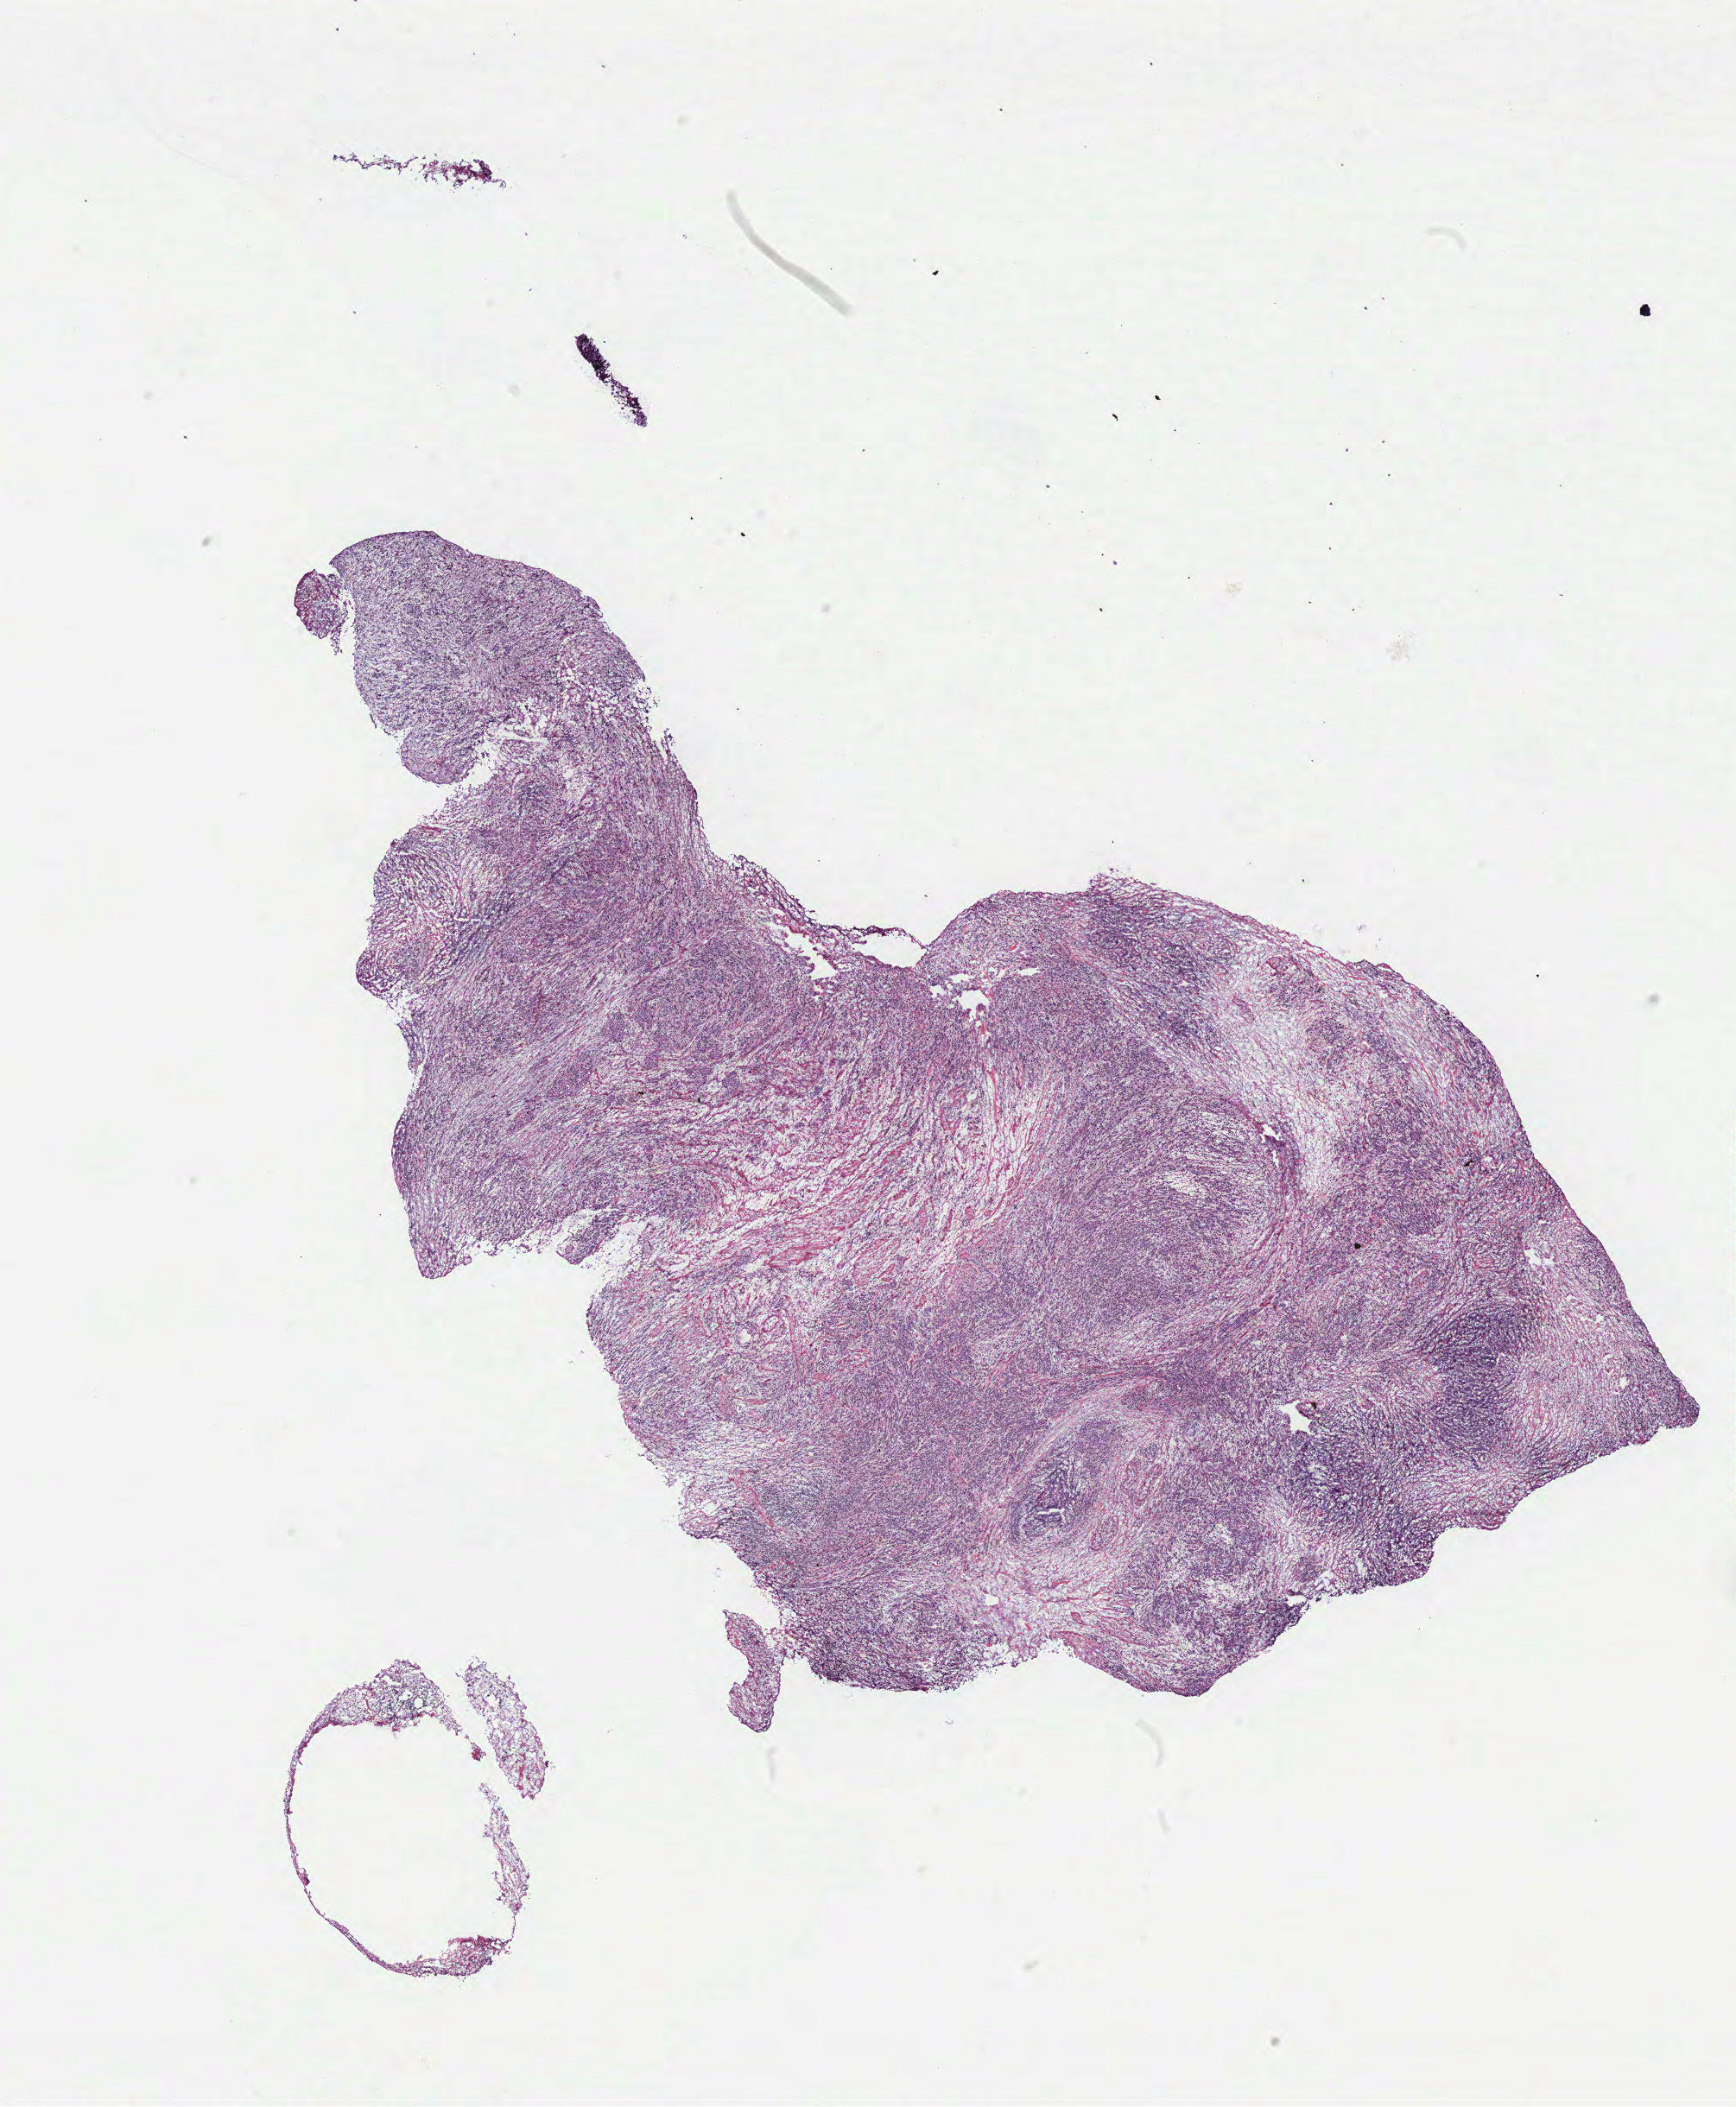
H&E whole-slide image, a low-resolution overview of the entire scanned area, about 16.1 x 19.5 mm; normal (non-tumour) tissue sample, colon. Patient: female, age 57 years.
* this section: normal (non-tumour) tissue from the same patient
* patient diagnosis: Adenocarcinoma, NOS